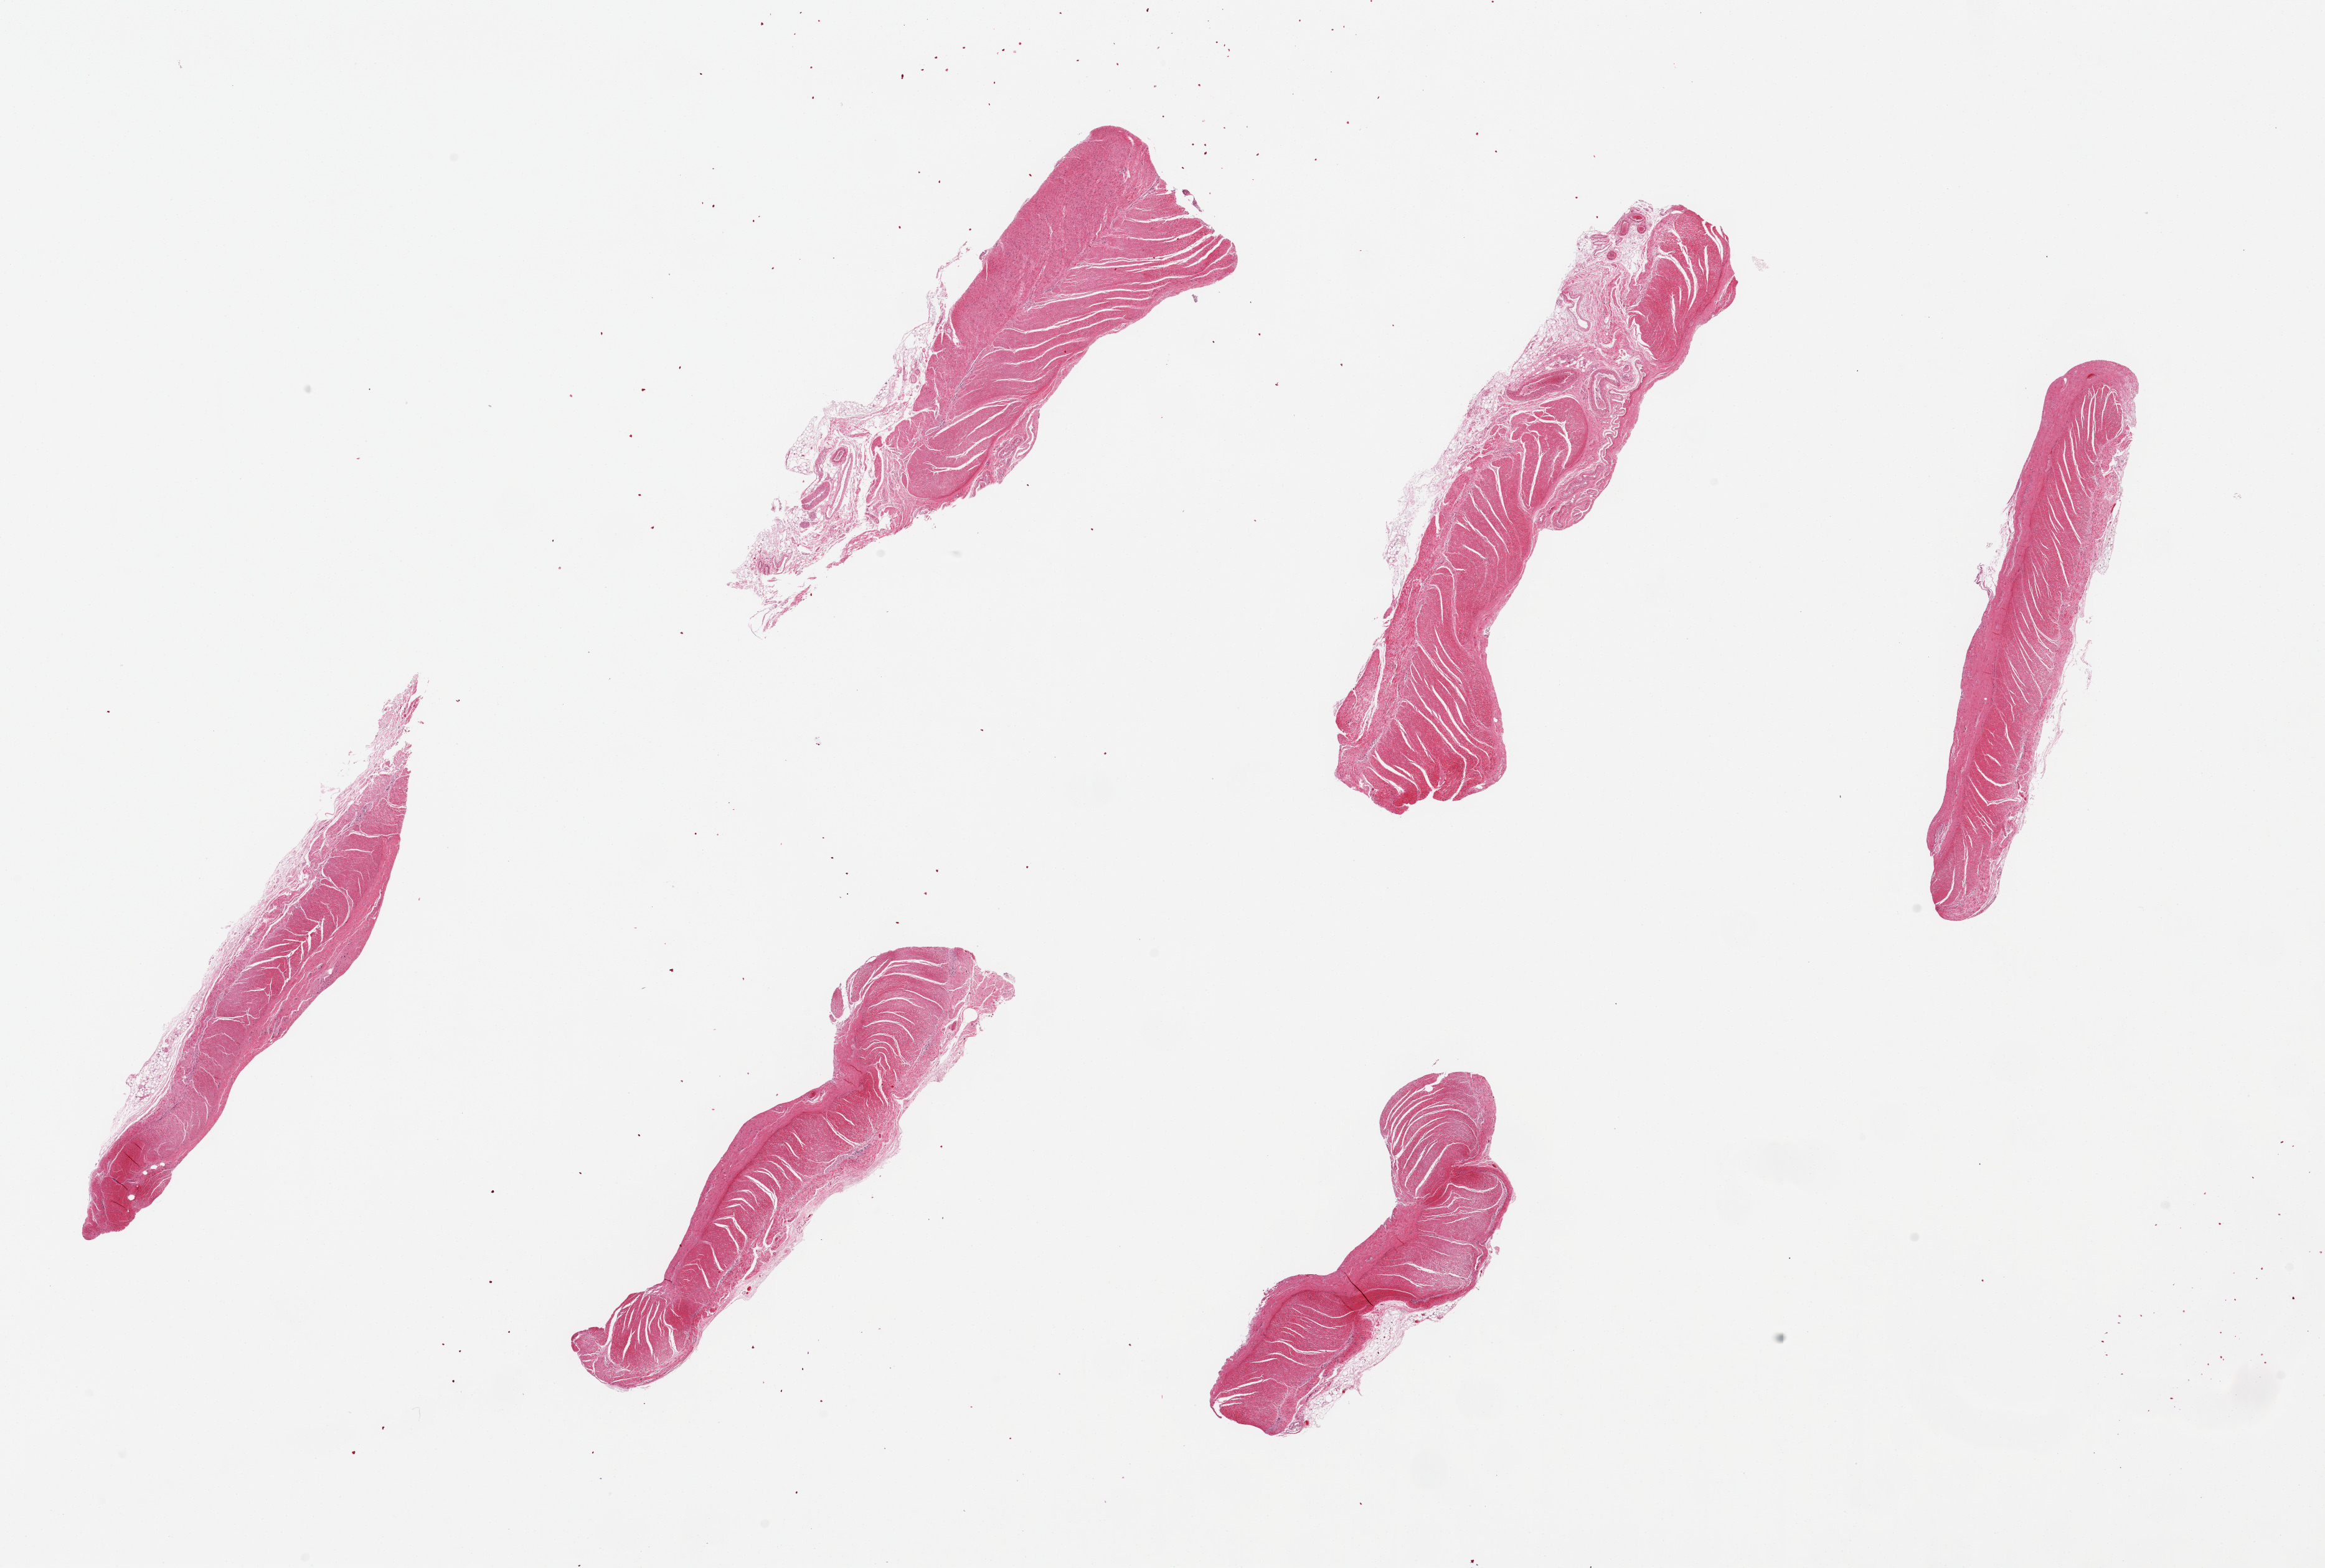
Digitized hematoxylin and eosin (H&E)-stained section — shown as a low-resolution overview of the whole scanned area (about 29.5 x 19.9 mm); PAXgene-fixed, paraffin-embedded tissue; sampled site (target tissue): sigmoid colon; tissue donor sample. Donor: male.
• pathologist's review note for this sample: 6 pieces up to 8.5x3mm; all muscularis